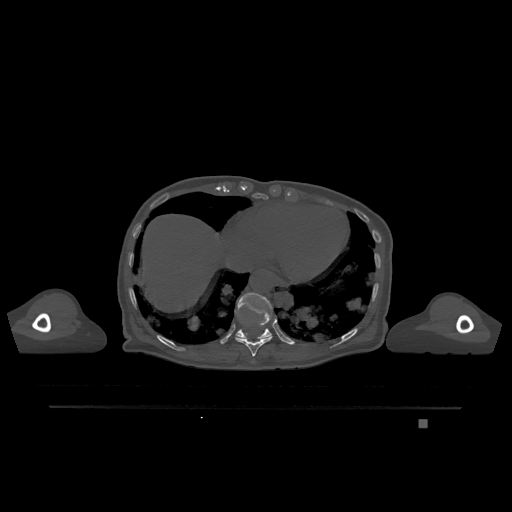
CT including the spine, one axial slice. Position 621 of 1317 along the scan axis. Bone window (W 1800 / L 400 HU). 0.5 mm slice thickness. 512 × 512 image matrix, field of view 500 × 500 mm. Female patient, age 74 years. Case-level facts recorded for this patient, not image findings: primary cancer: lung; vertebrae with lytic lesions (as recorded): T1, T4, T5, T6, L4, L5.
Outlined on this slice (semi-automatically segmented with operator editing):
- T10 vertebra: bounding box [x1, y1, x2, y2] px = [235, 334, 272, 357]
- T11 vertebra: [235, 292, 276, 339]